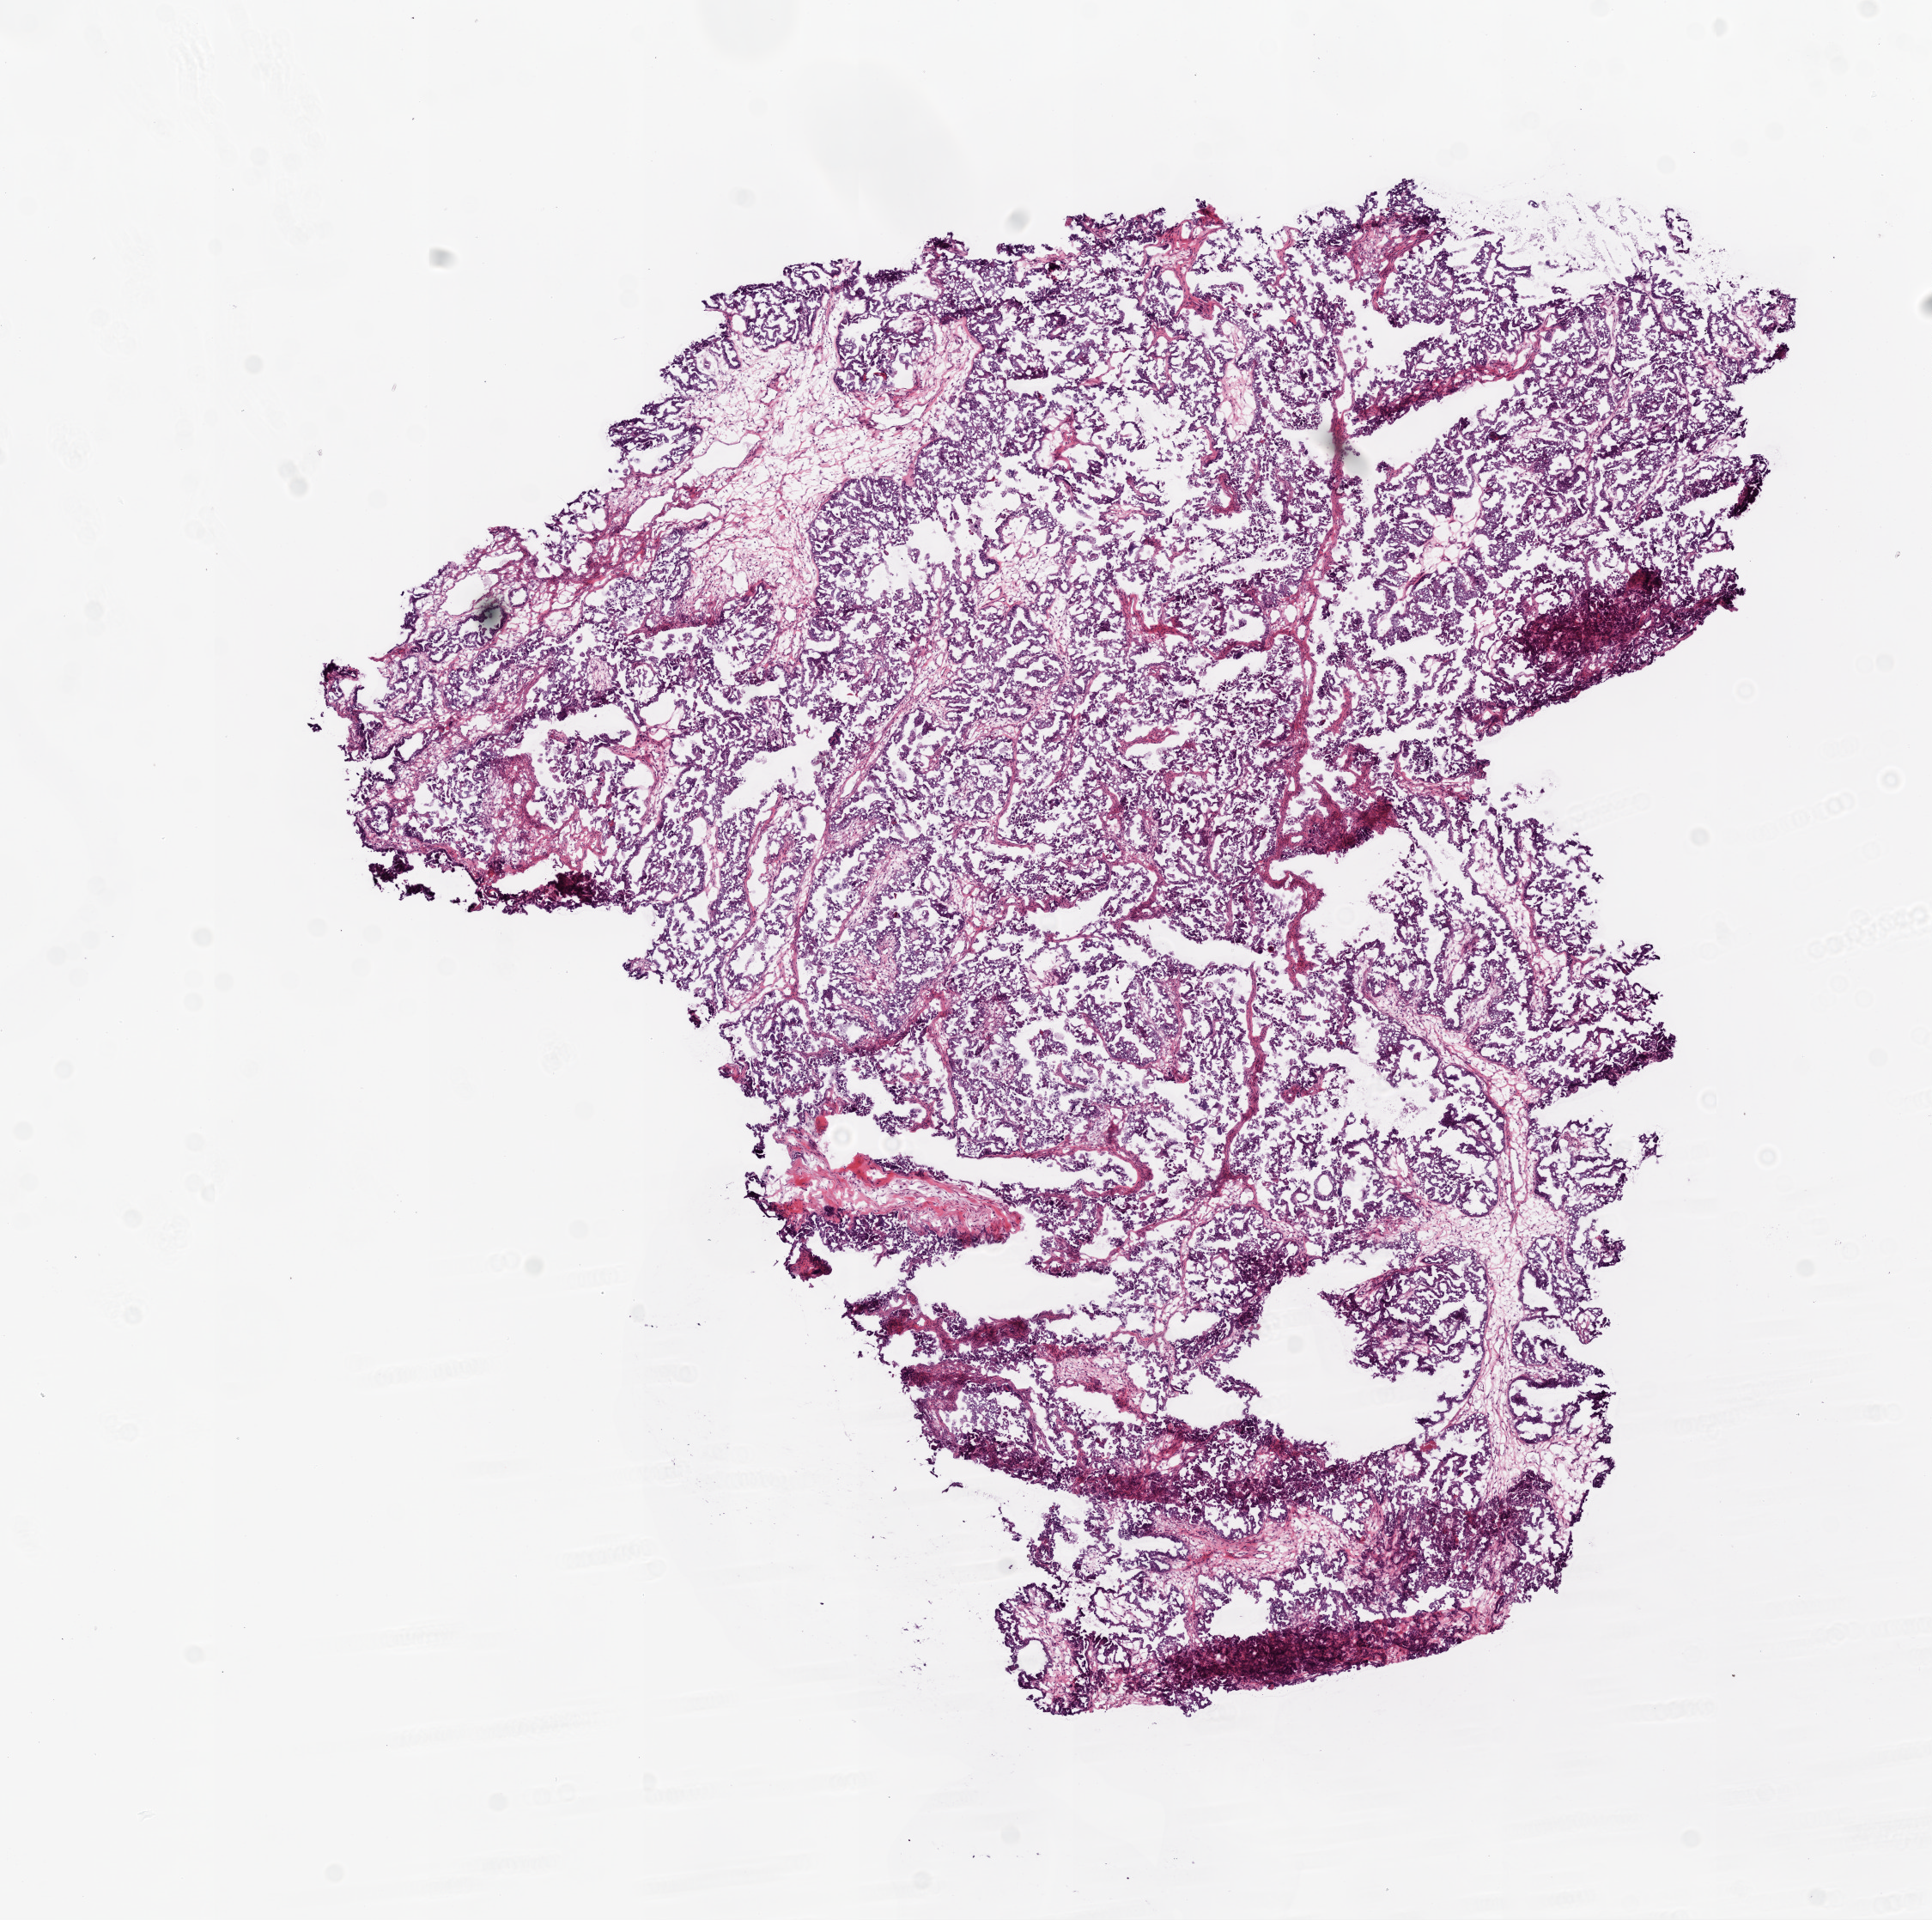
H&E-stained whole-slide image, low-resolution overview of the scanned area, about 9.0 x 9.0 mm. Frozen section. Sample: primary tumour, ovary. Female, age 56 years at initial diagnosis. Histologic grade: G3 (poorly differentiated). Composition of this section per pathologist review: tumour cells 90%, tumour nuclei 97%, normal cells 8%, stromal cells 0%, necrosis 2%.
Diagnosis: Serous cystadenocarcinoma, NOS. FIGO stage: IIIC.